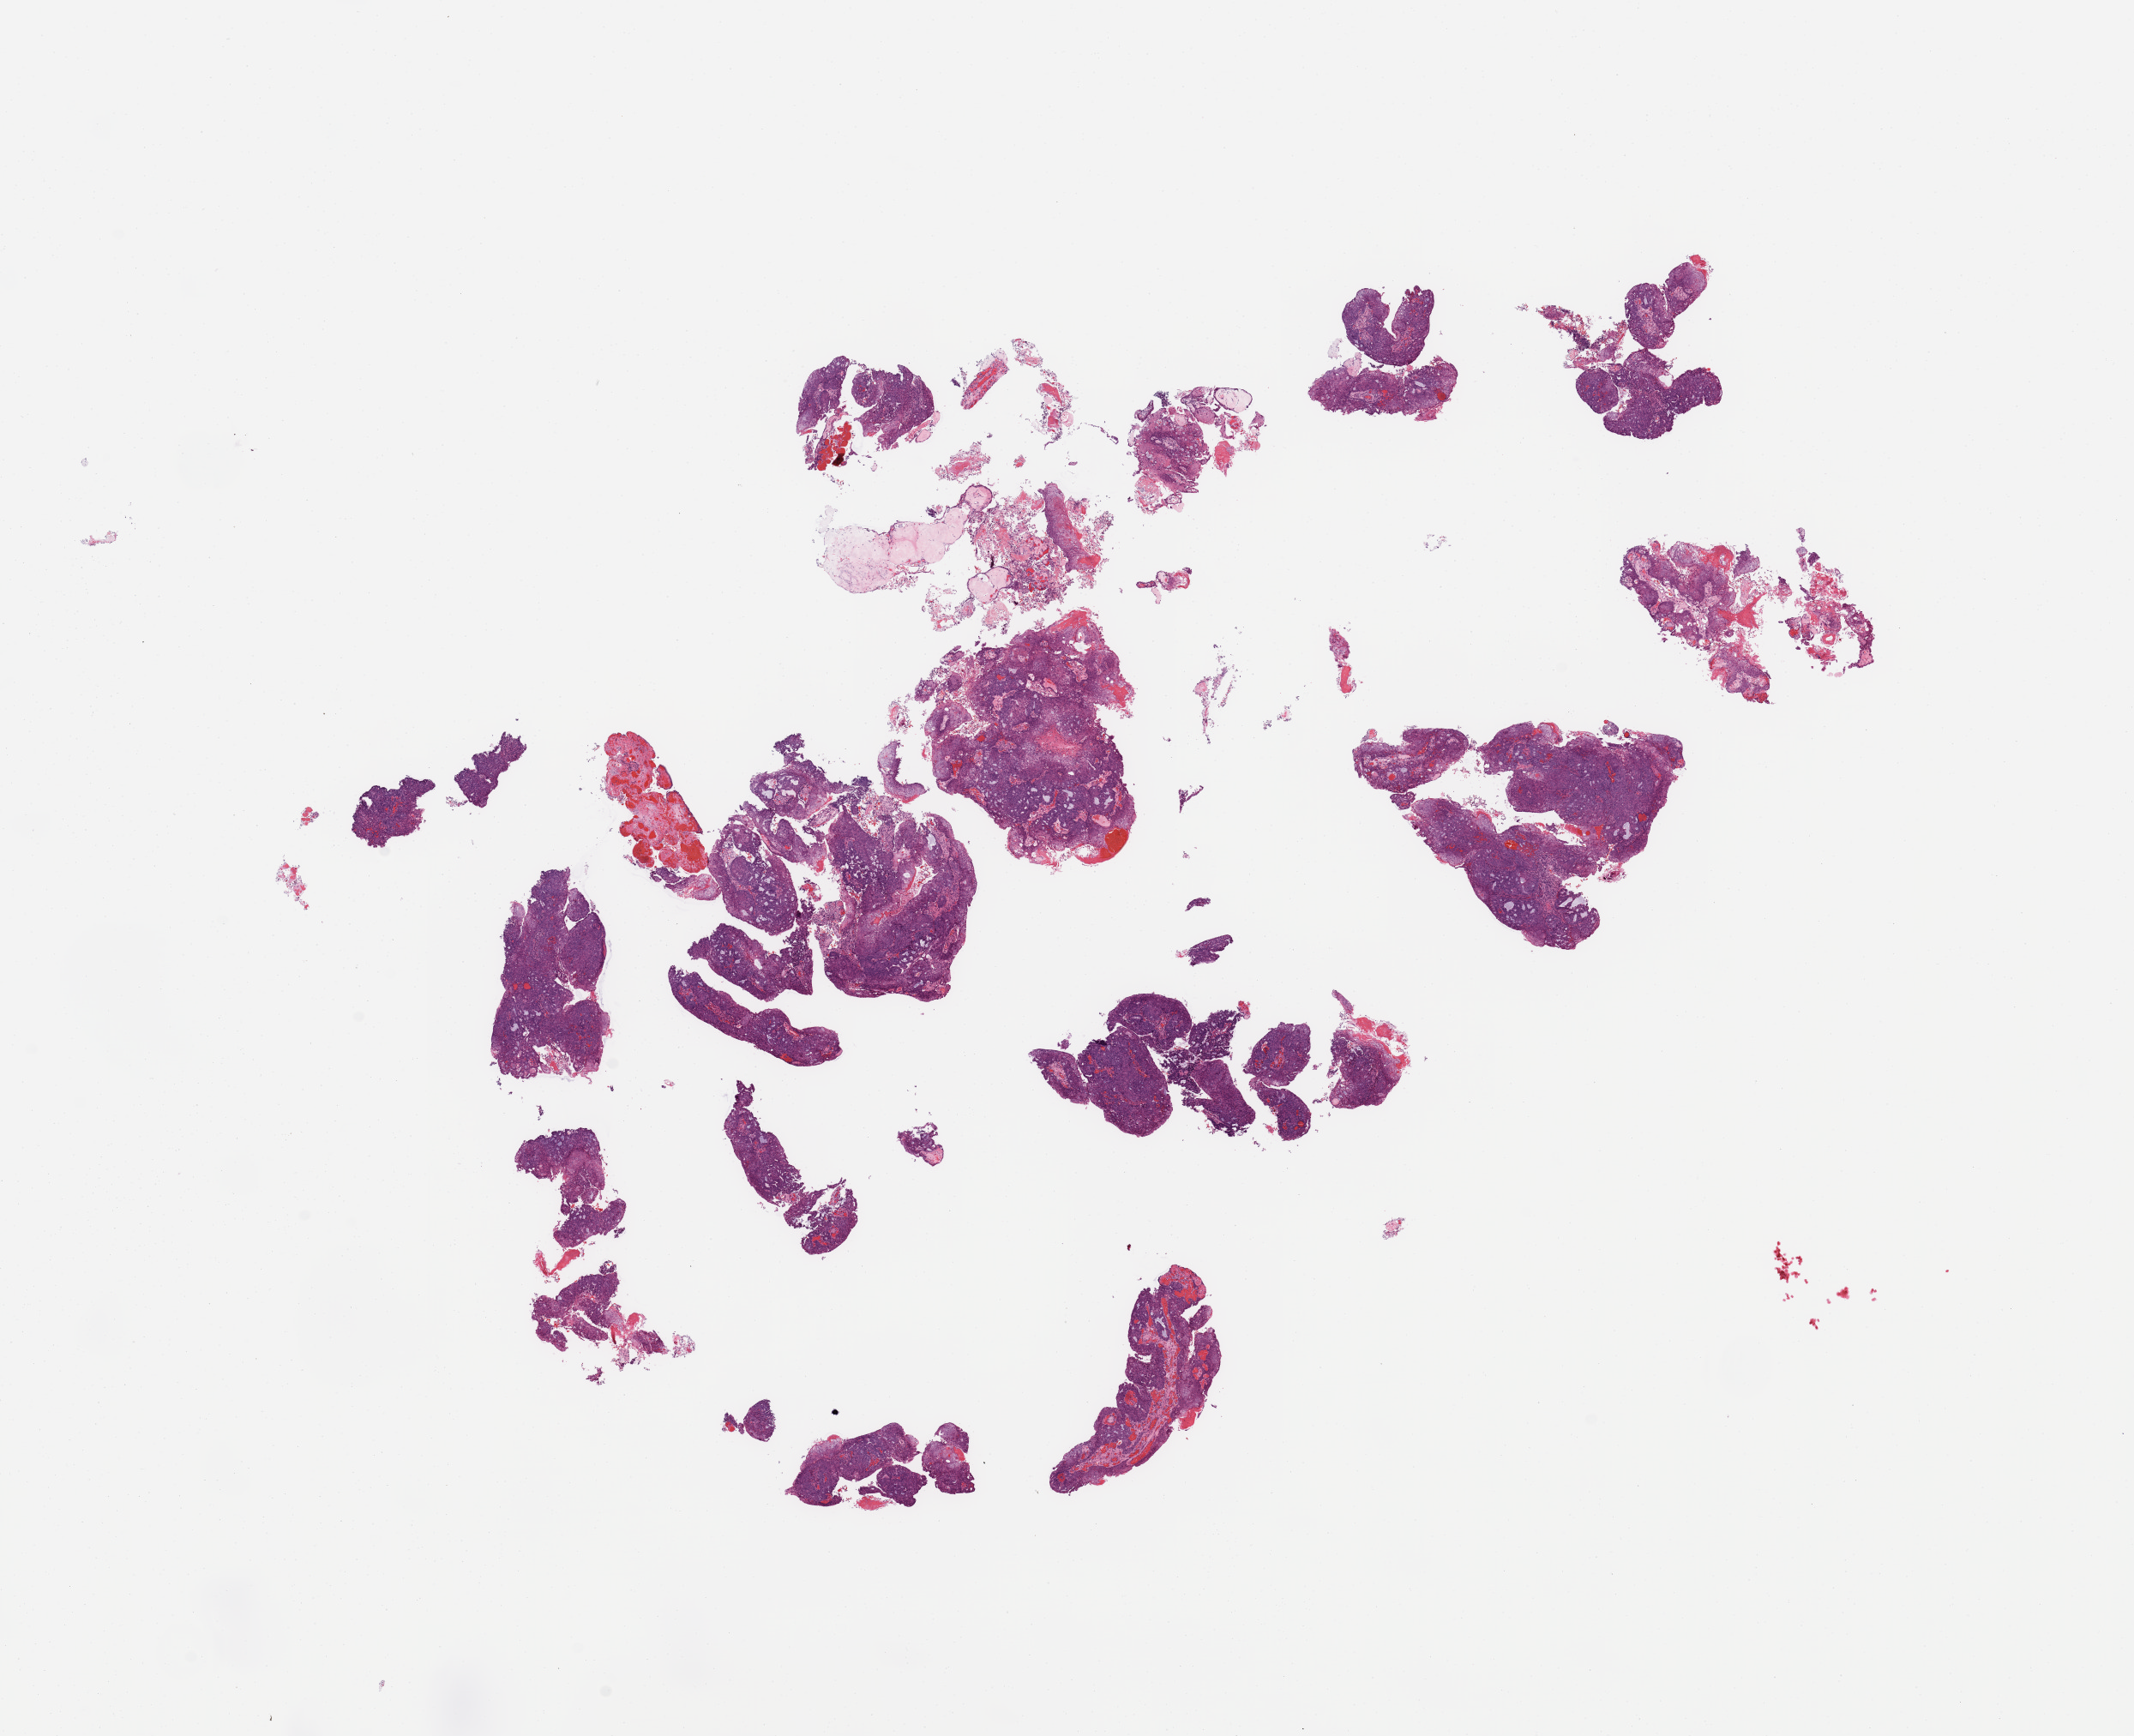
Whole-slide histology image, H&E-stained — whole scanned area (about 19.7 x 16.0 mm, slide scanned at 20x) shown as a low-resolution overview. Uterus, tumour tissue. Female, 60 y/o.
Diagnosis: Endometrioid adenocarcinoma, NOS.